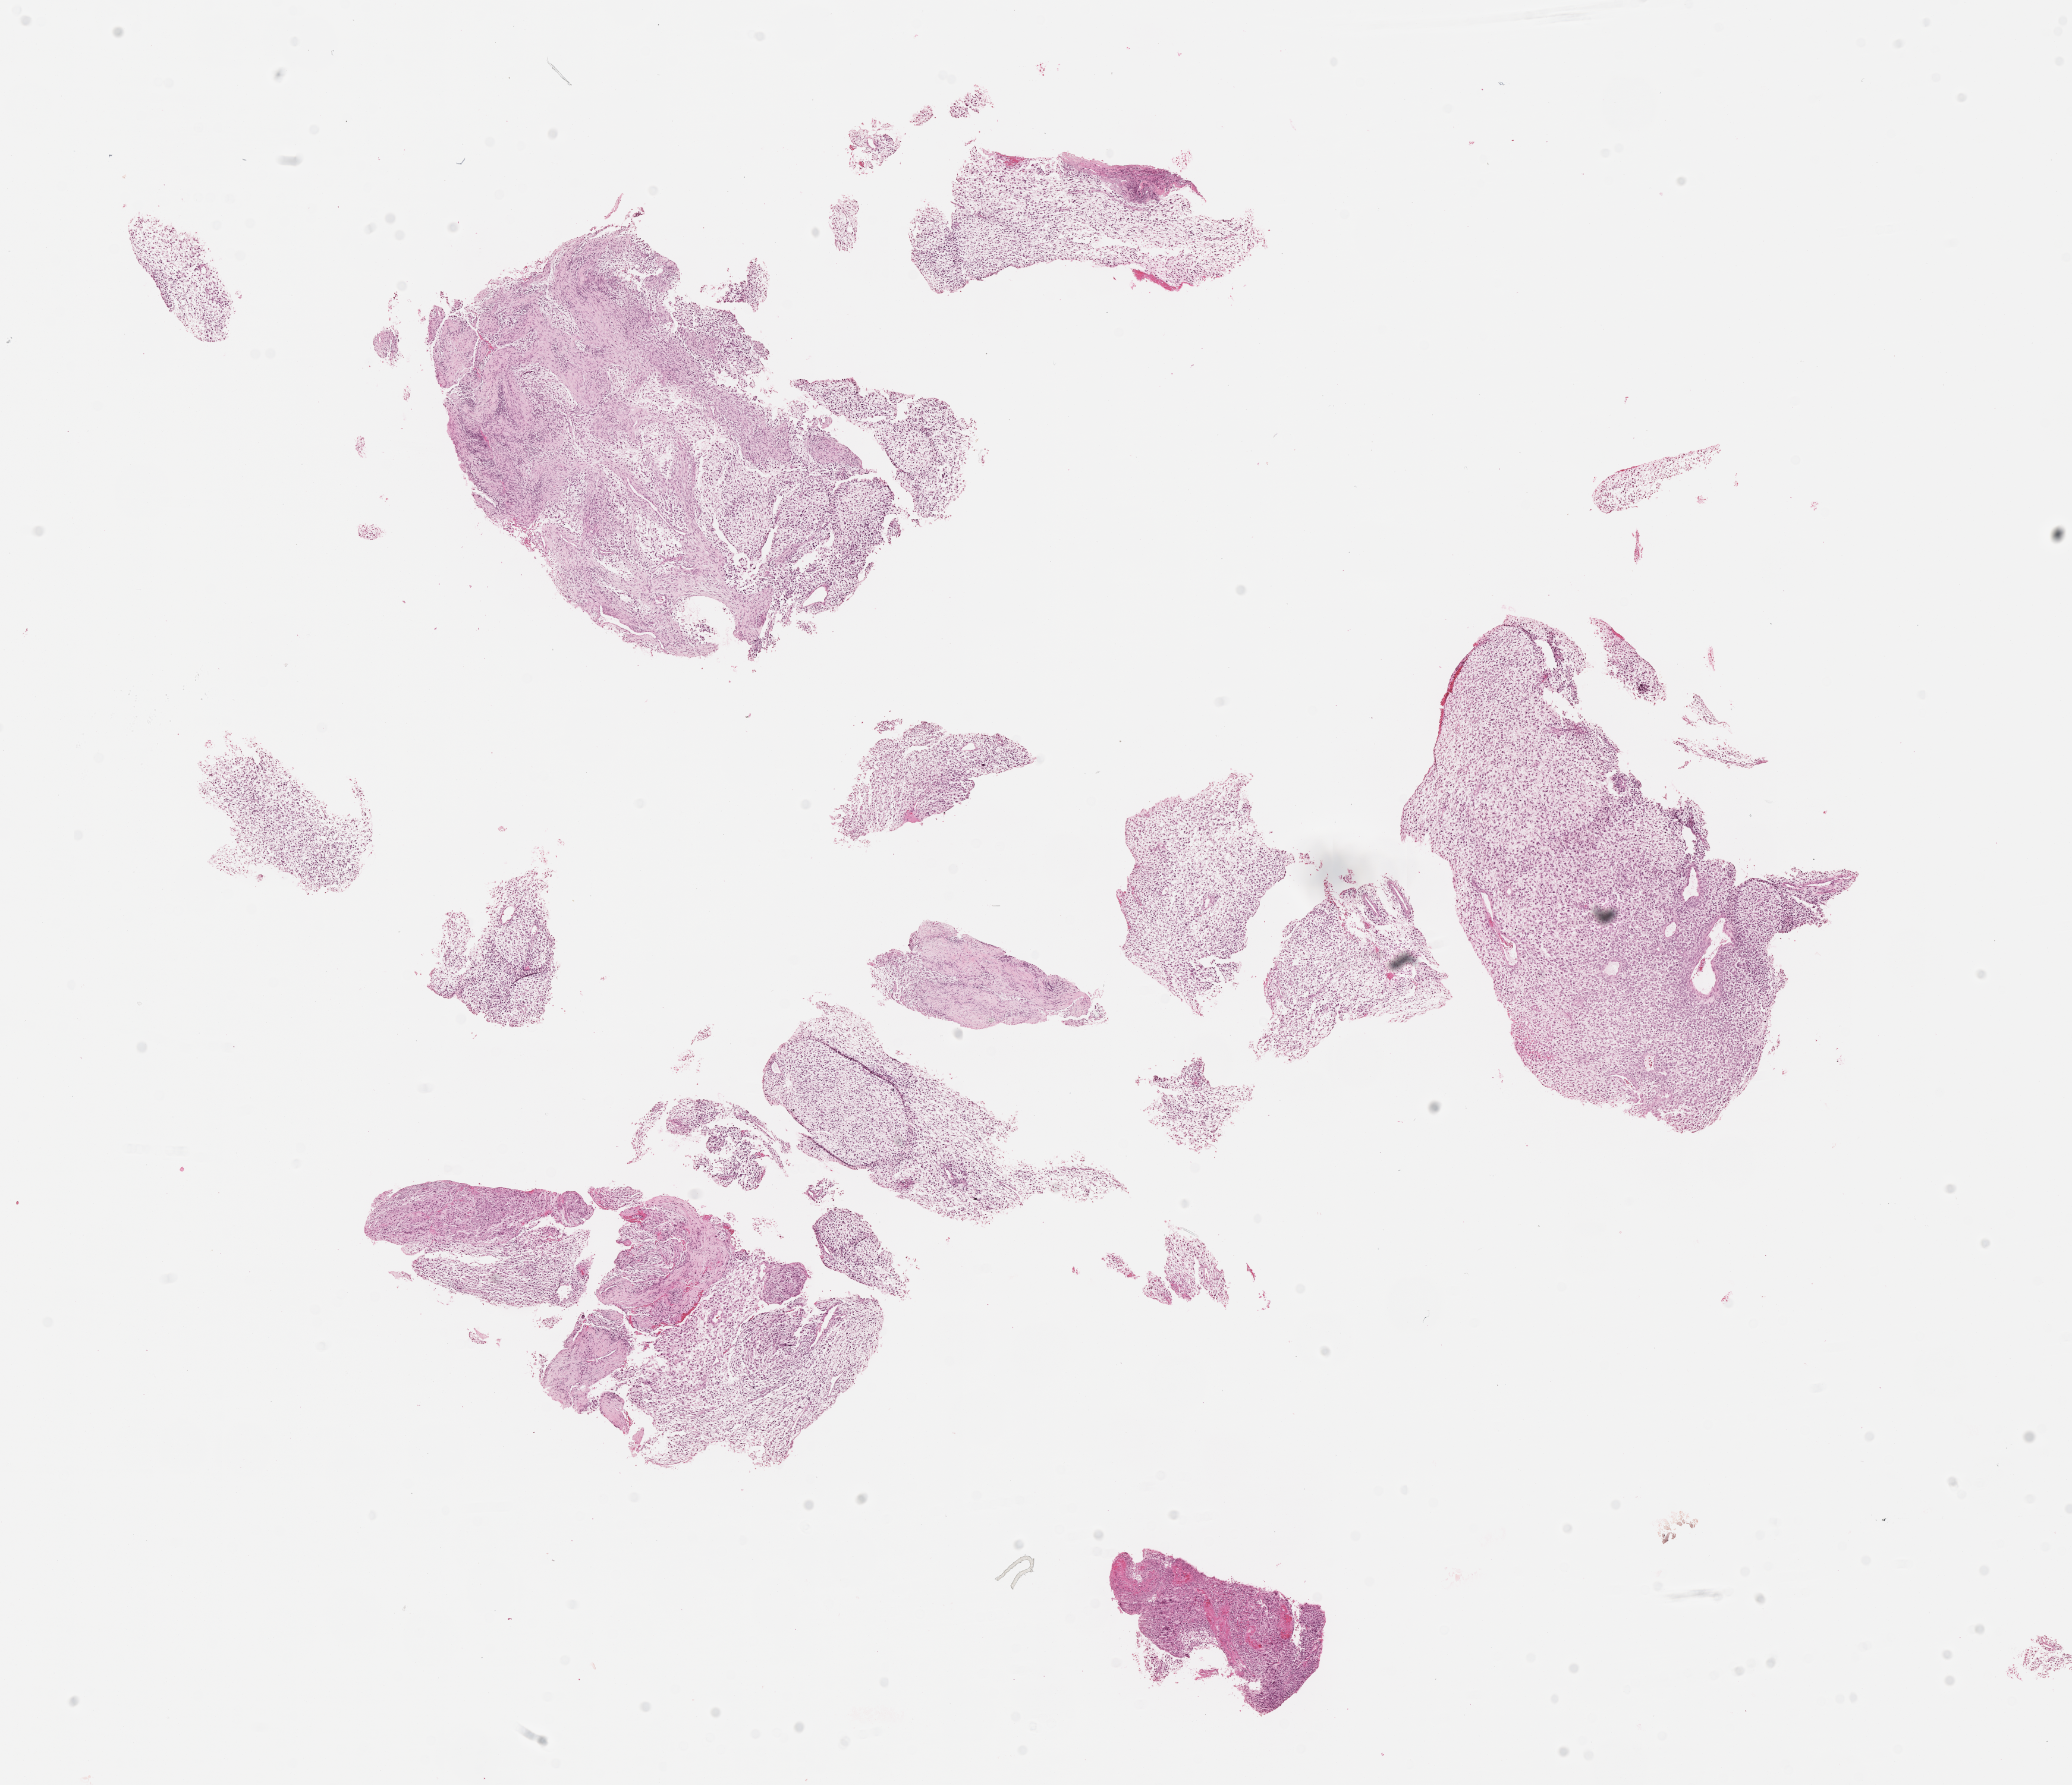
Digitized H&E-stained section of tumor tissue, a low-resolution overview of the entire scanned area, about 14.1 x 12.1 mm; formalin-fixed paraffin-embedded section; sample anatomic site: cheek, left. Male patient, age at diagnosis 3.1 years.
Diagnosis: rhabdomyosarcoma; histological classification: embryonal rhabdomyosarcoma. Stage (as recorded): 1. Metastatic status at presentation (as recorded): non-metastatic (confirmed).